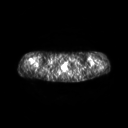
FDG PET of an extremity soft-tissue mass (from a PET/CT study), one axial slice. 3.27 mm slice thickness. 128 × 128 image matrix, field of view 600 × 600 mm. Female patient, age 28 years. From the clinical record (not read from this slice): histological type: malignant fibrous histiocytoma; grade: low; site of the primary tumour: left arm.
Structures marked on this image (expert contour drawn on MRI and transferred to this co-registered scan by the dataset authors):
- gross tumour volume (mass): bounding box [x1, y1, x2, y2] px = [99, 66, 102, 69]